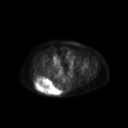
FDG PET of an extremity soft-tissue mass (from a PET/CT study), one axial slice; position 63 of 267 along the scan axis; 3.27 mm slice thickness; 128 × 128 image matrix, field of view 600 × 600 mm. Female patient, age 60 years. From the clinical record (not read from this slice): histological type: spindle cell suggestive of myxofibrosarcoma; grade: intermediate; site of the primary tumour: right buttock.
Outlined on this slice (expert contour drawn on MRI and transferred to this co-registered scan by the dataset authors):
- gross tumour volume (mass): bounding box <35,77,62,96> (left, top, right, bottom; pixels)